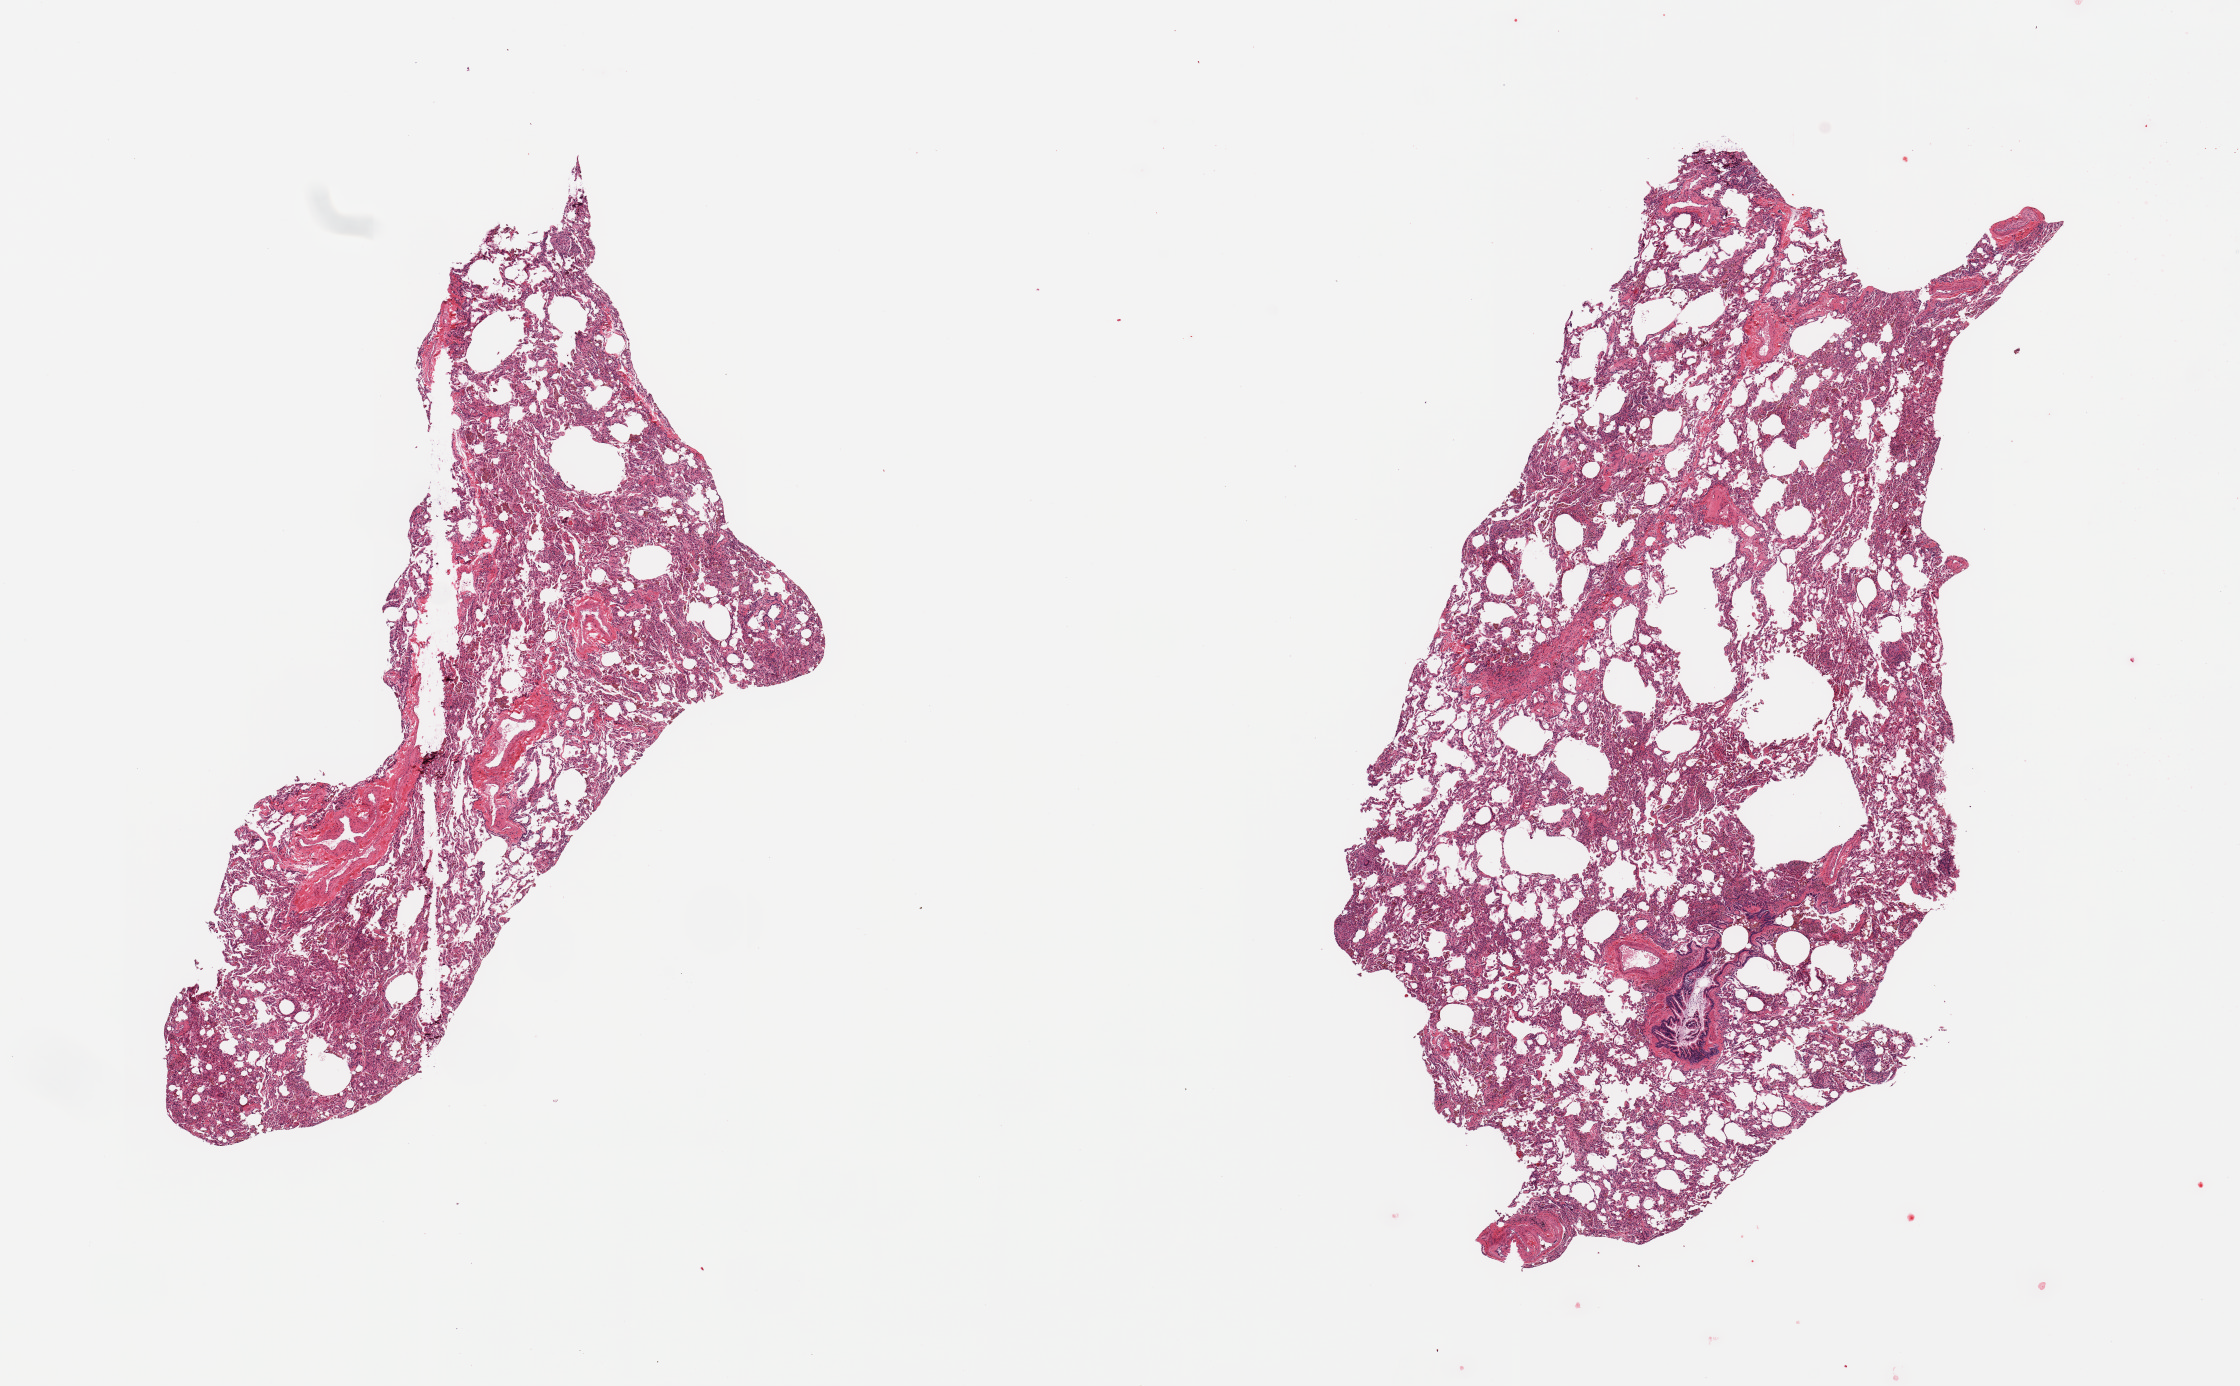
Hematoxylin and eosin (H&E) whole-slide image, shown as a low-resolution overview of the whole scanned area (about 17.7 x 11.0 mm, slide scanned at 20x). PAXgene-fixed paraffin-embedded (PFPE) section. Sampled site (target tissue): lung. Tissue donor sample. Donor: male.
• reviewer comment on this tissue sample: 2 pieces; pigmented macrophages and patchy atelectasis, rare giant cell (?aspiration)